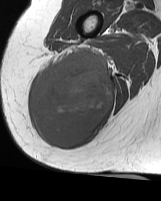
MRI of an extremity soft-tissue mass, one axial slice; MR volume resampled by the dataset authors to the PET/CT grid (not the native acquisition matrix); 3.27 mm slice thickness; 161 × 201 image matrix. Female patient. Case-level facts recorded for this patient, not image findings: histological type: synovial sarcoma; grade: intermediate; site of the primary tumour: right buttock.
Outlined on this slice (expert contour drawn on MRI and transferred to this co-registered scan by the dataset authors):
- gross tumour volume including surrounding oedema: box from (x=31, y=49) to (x=114, y=148) px
- gross tumour volume (mass): (x=31, y=49)–(x=114, y=148)